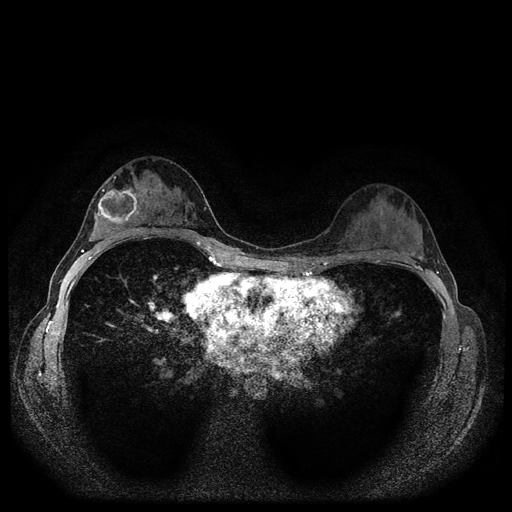
Breast MRI (dynamic contrast-enhanced, multi-phase), one axial slice; position 63 of 116 along the scan axis; dynamic contrast-enhanced series, time point 2 of 5 at this slice position (early post-contrast); 1.5 T; TE 2.7 ms, TR 5.4 ms; 2 mm slice thickness; 512 × 512 image matrix, field of view 320 × 320 mm. Female patient, age 29 years.
Structures marked on this image (semi-automatic segmentation, software-assisted and operator-edited):
- breast lesion (labelled 'tumour' in the annotation; benign lesions carry a separate 'benign' label): bounding box [x1, y1, x2, y2] px = [95, 186, 140, 227]